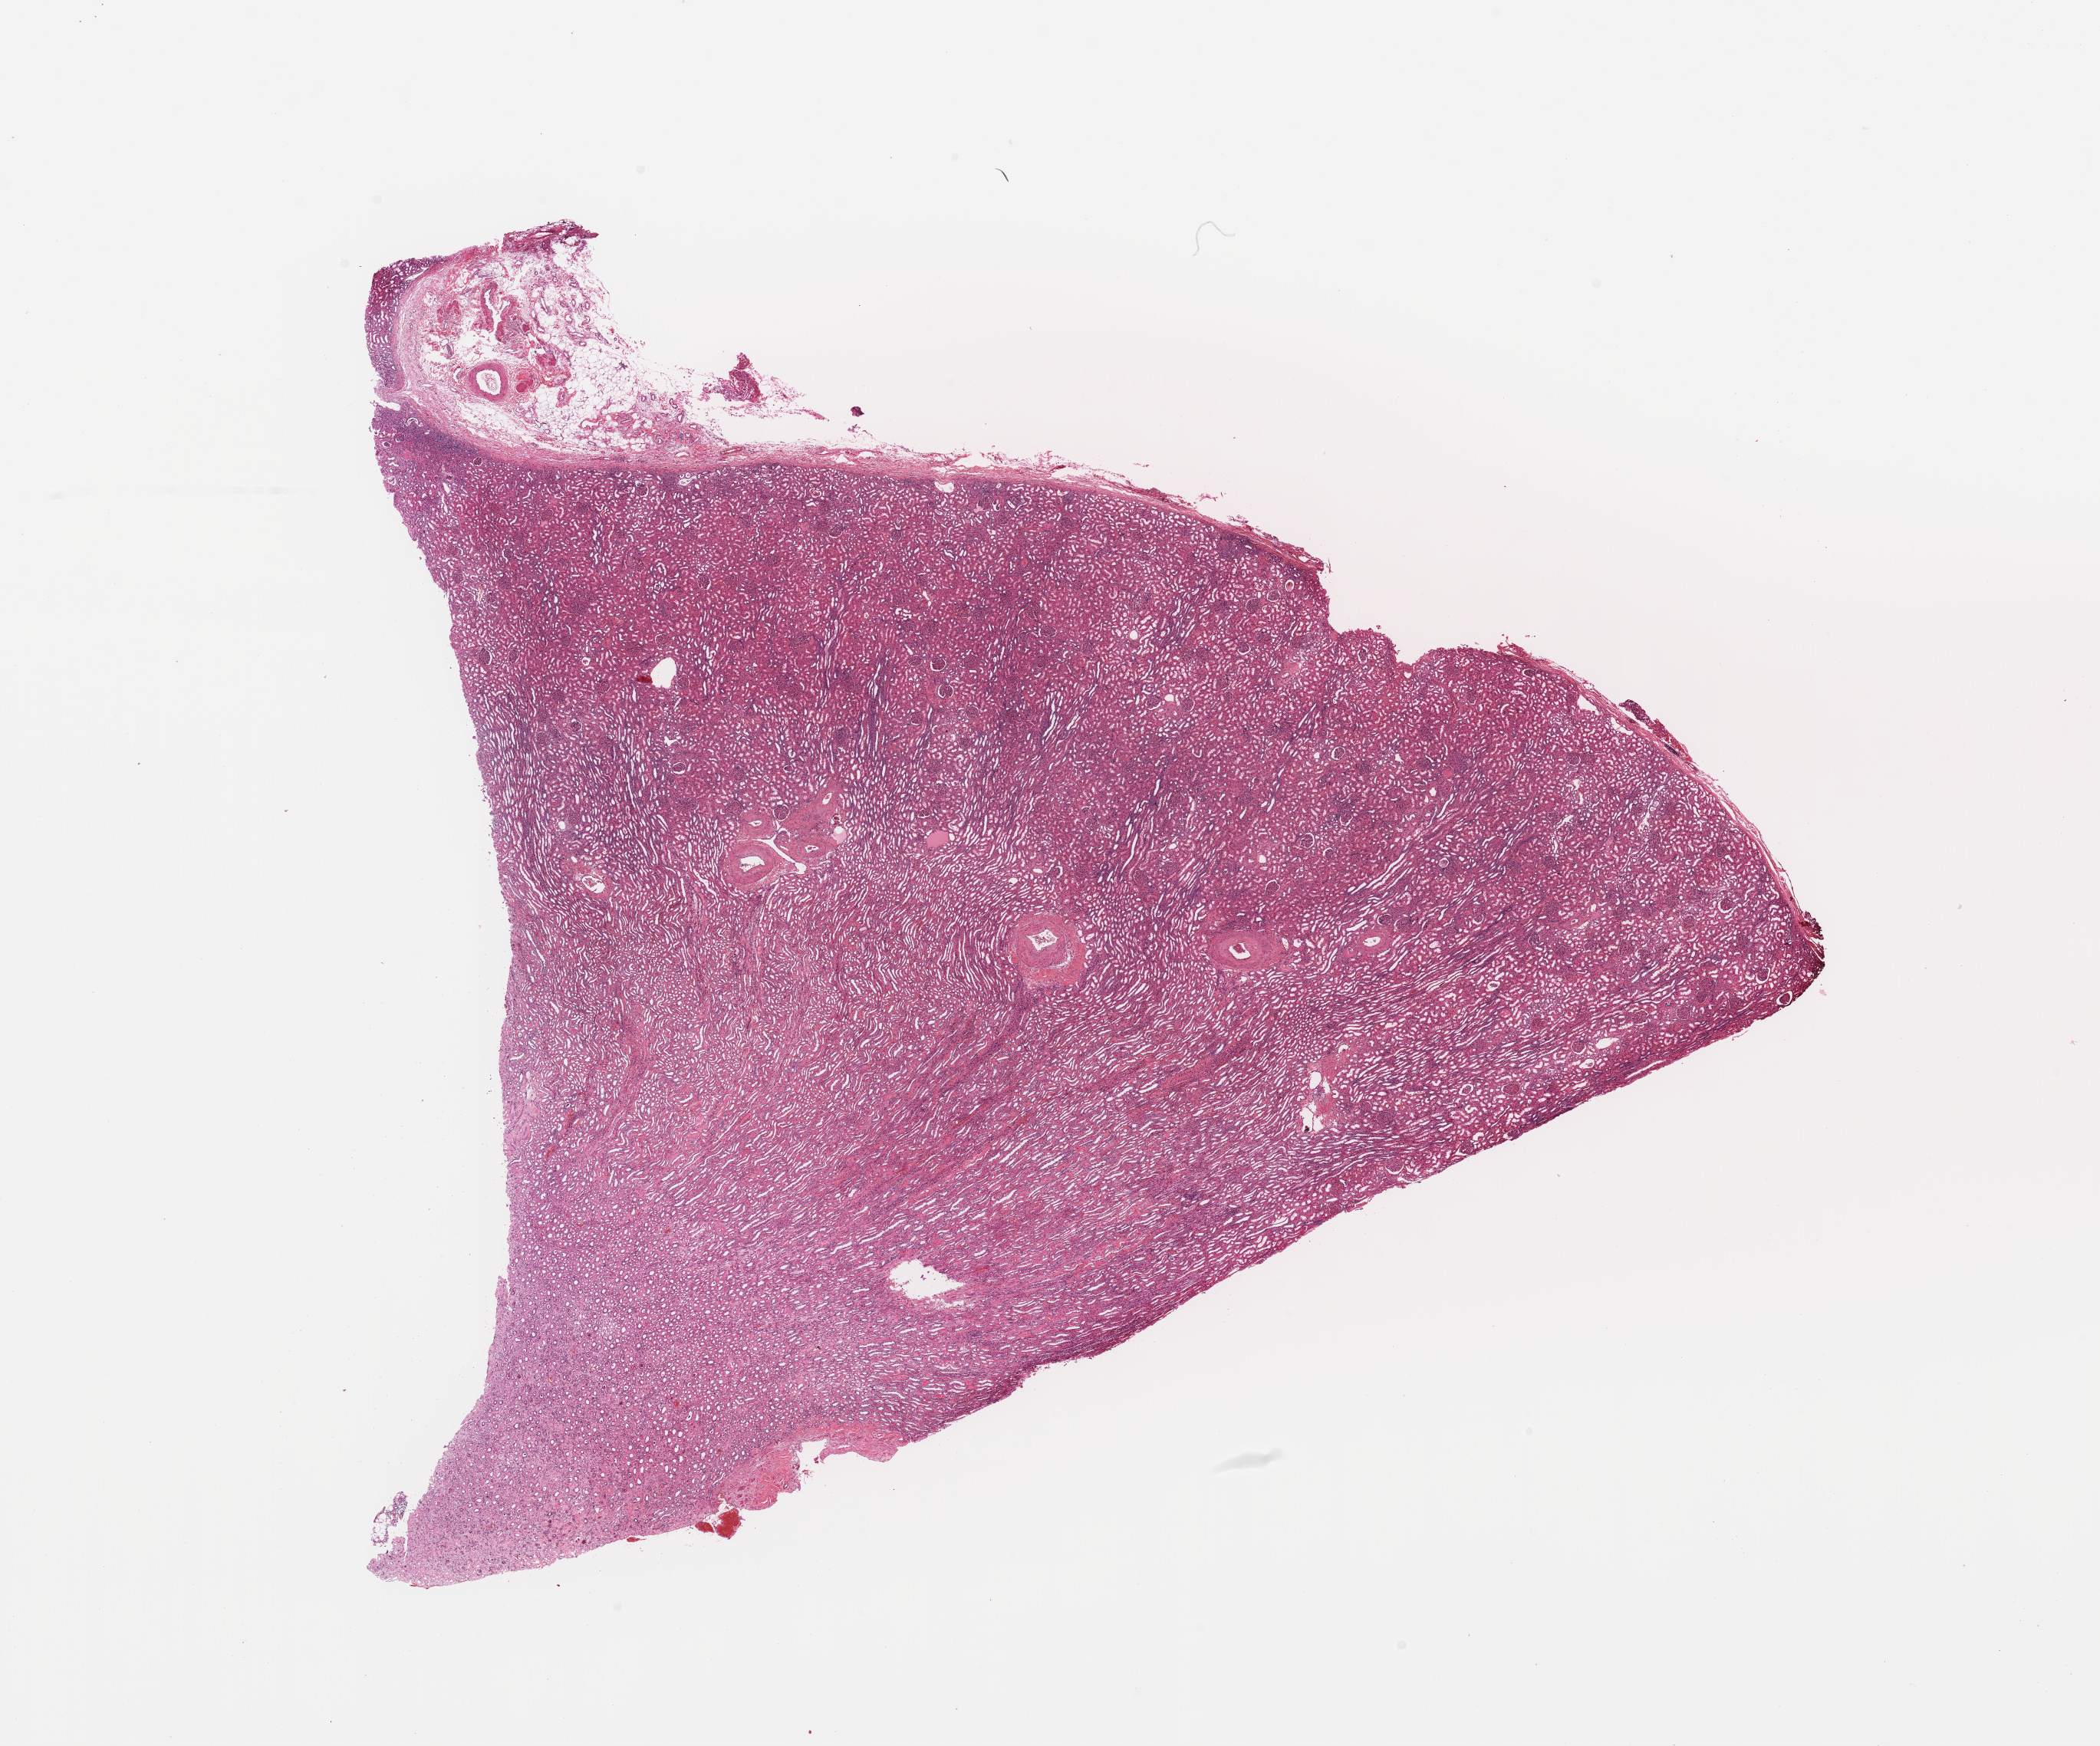
H&E whole-slide image, low-resolution overview of the scanned area, about 21.7 x 18.0 mm (acquisition: 20x scan). Normal (non-tumour) tissue sample, sampled site: kidney. Patient: male, age 63 years.
This section: normal (non-tumour) tissue from the same patient. Patient diagnosis: Renal cell carcinoma, NOS.